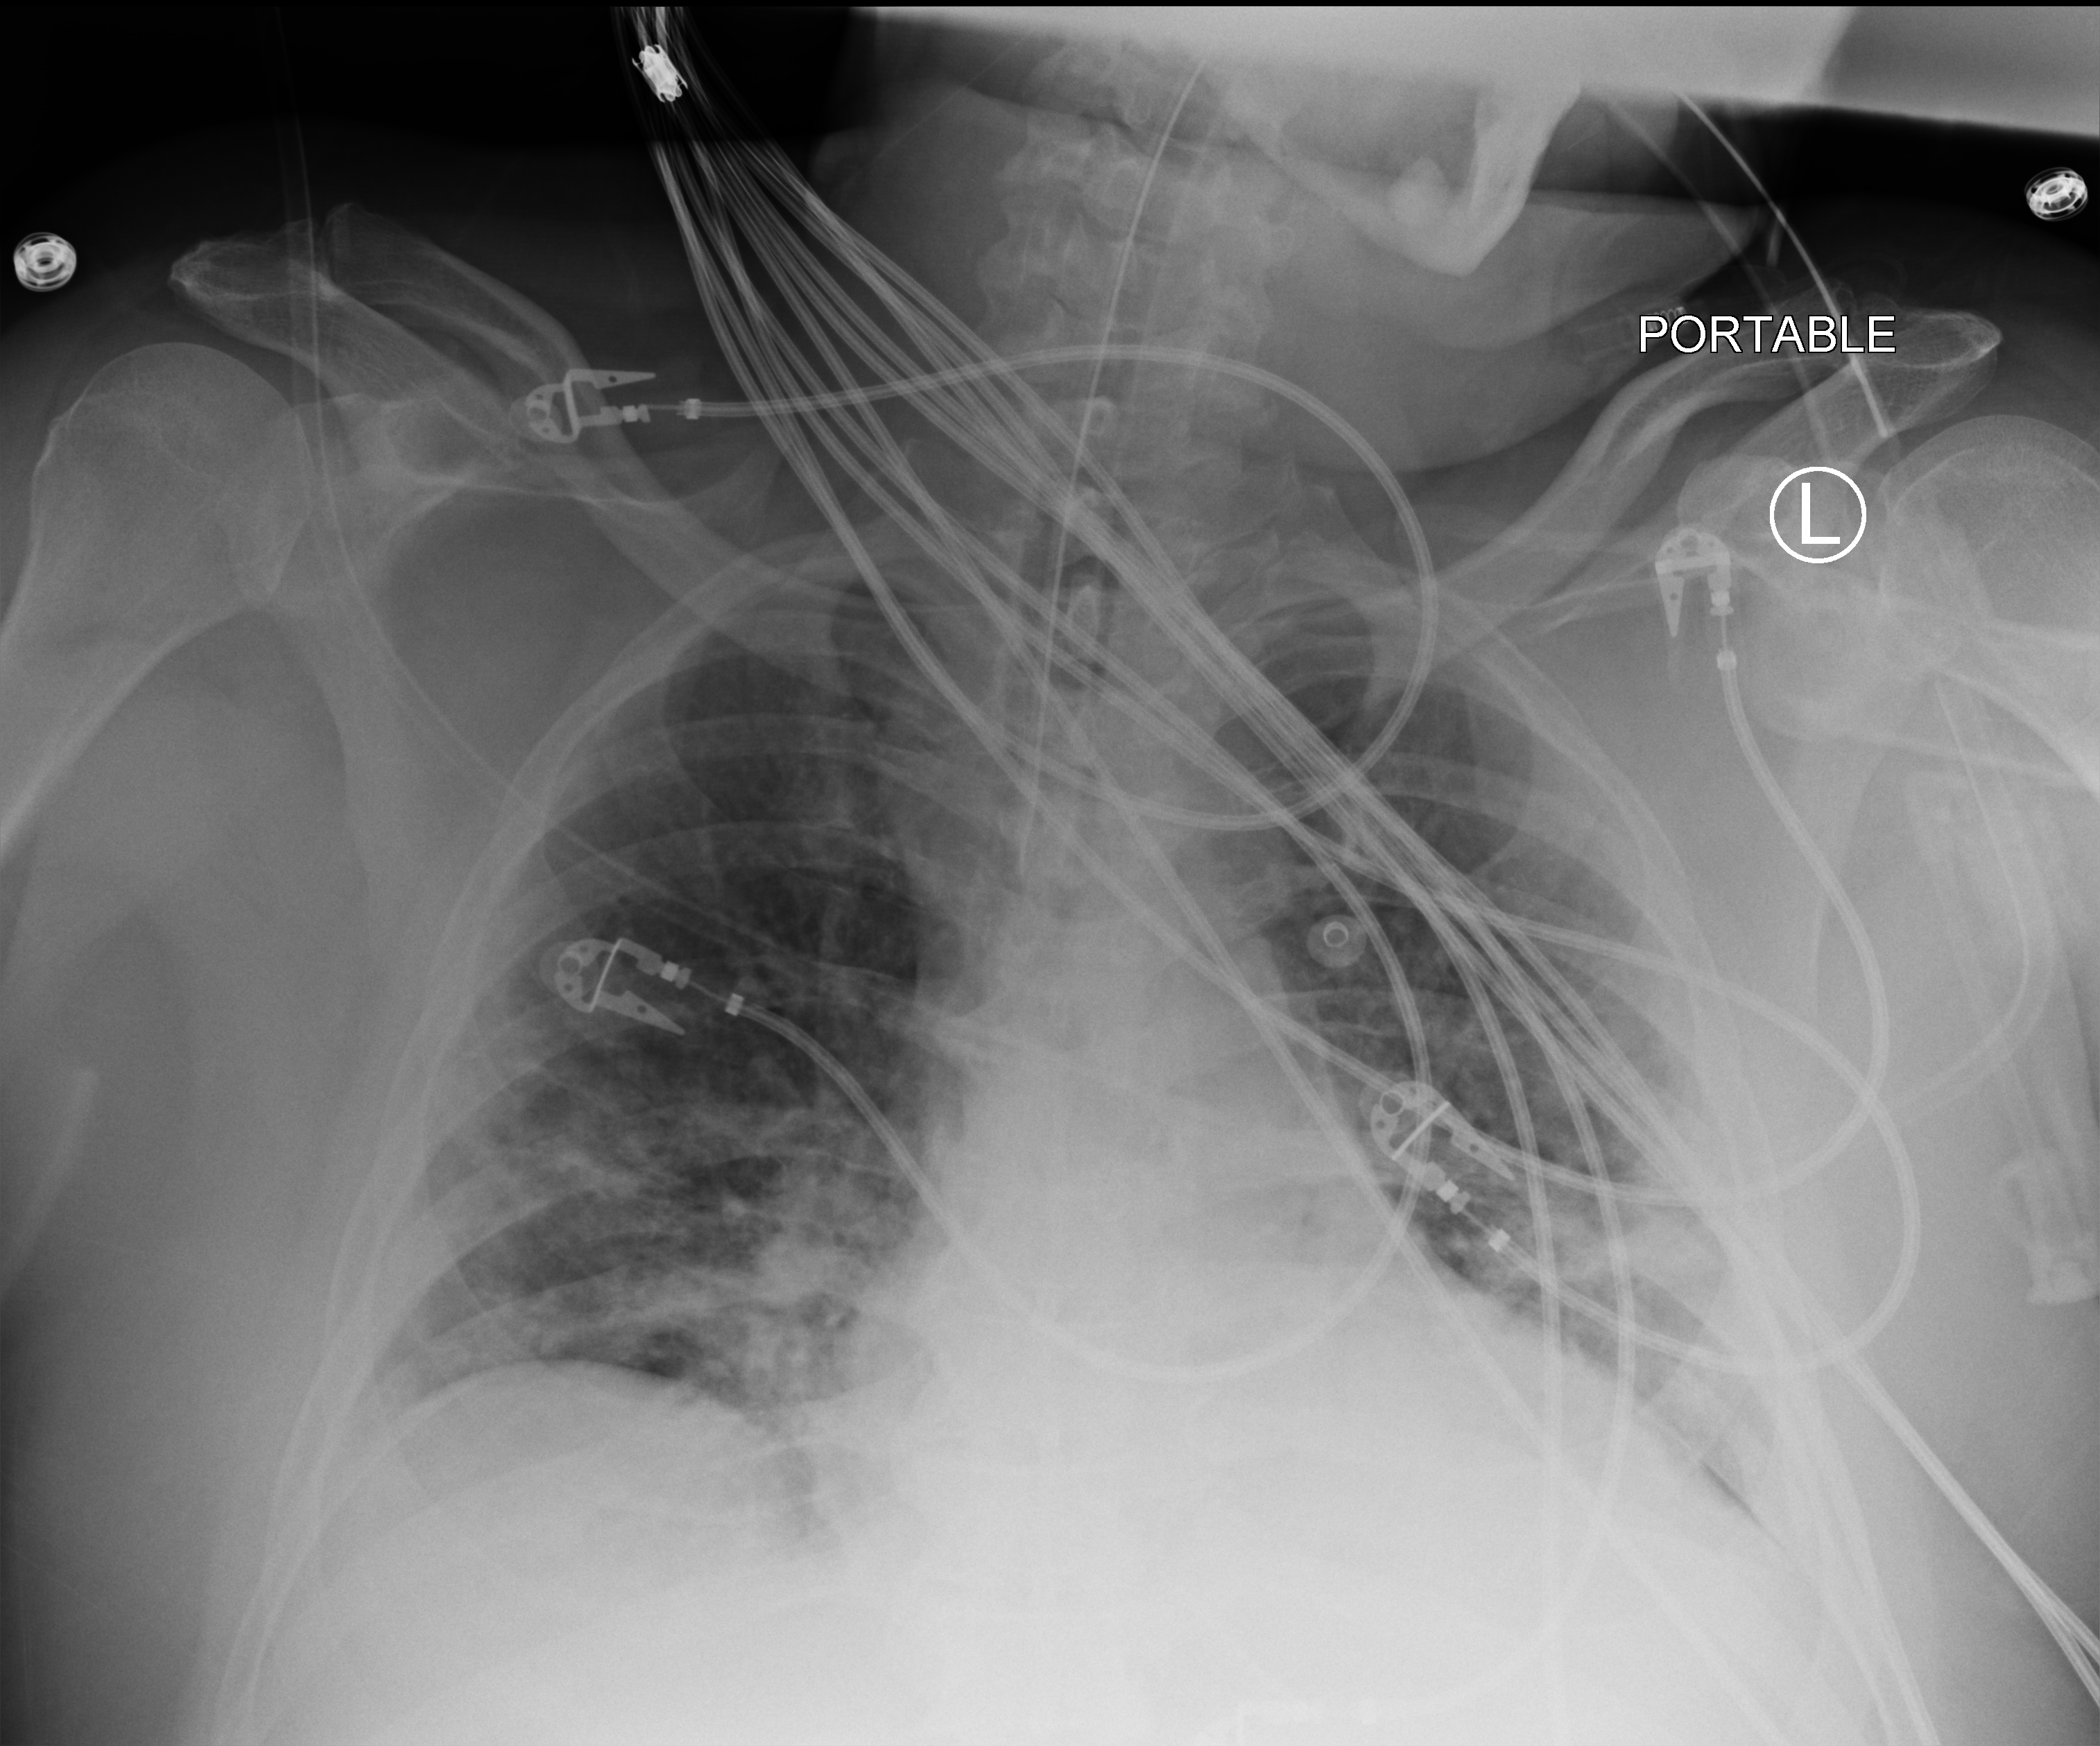
Chest X-ray (portable); anteroposterior (AP) projection. Patient hospitalised with COVID-19; male, aged 18–59 years.
Admission-level facts for this patient (not findings on this image; timing relative to this image not recorded):
- admitted to intensive care during this hospital stay: yes